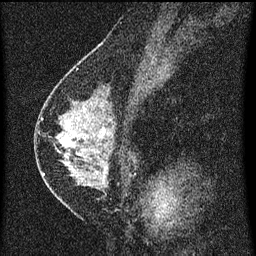
Breast MRI (dynamic contrast-enhanced), one sagittal slice; position 32 of 60 along the scan axis; dynamic contrast-enhanced series, image 2 of 3 at this slice position (ordered by acquisition); 1.5 T; TE 4.2 ms, TR 8 ms; 2 mm slice thickness; 256 × 256 image matrix. Female patient, age 47 years.
Annotated regions visible in this slice (semi-automatic segmentation, software-assisted and operator-edited):
- analysis volume of interest (the breast-tissue region the enhancement analysis was run in; not a lesion): bounding box (x1, y1, x2, y2) in pixels: (42, 92, 140, 199)
- tumour enhancement mask (voxels above the 70 % enhancement threshold inside the analysis volume of interest): (43, 124, 108, 177)